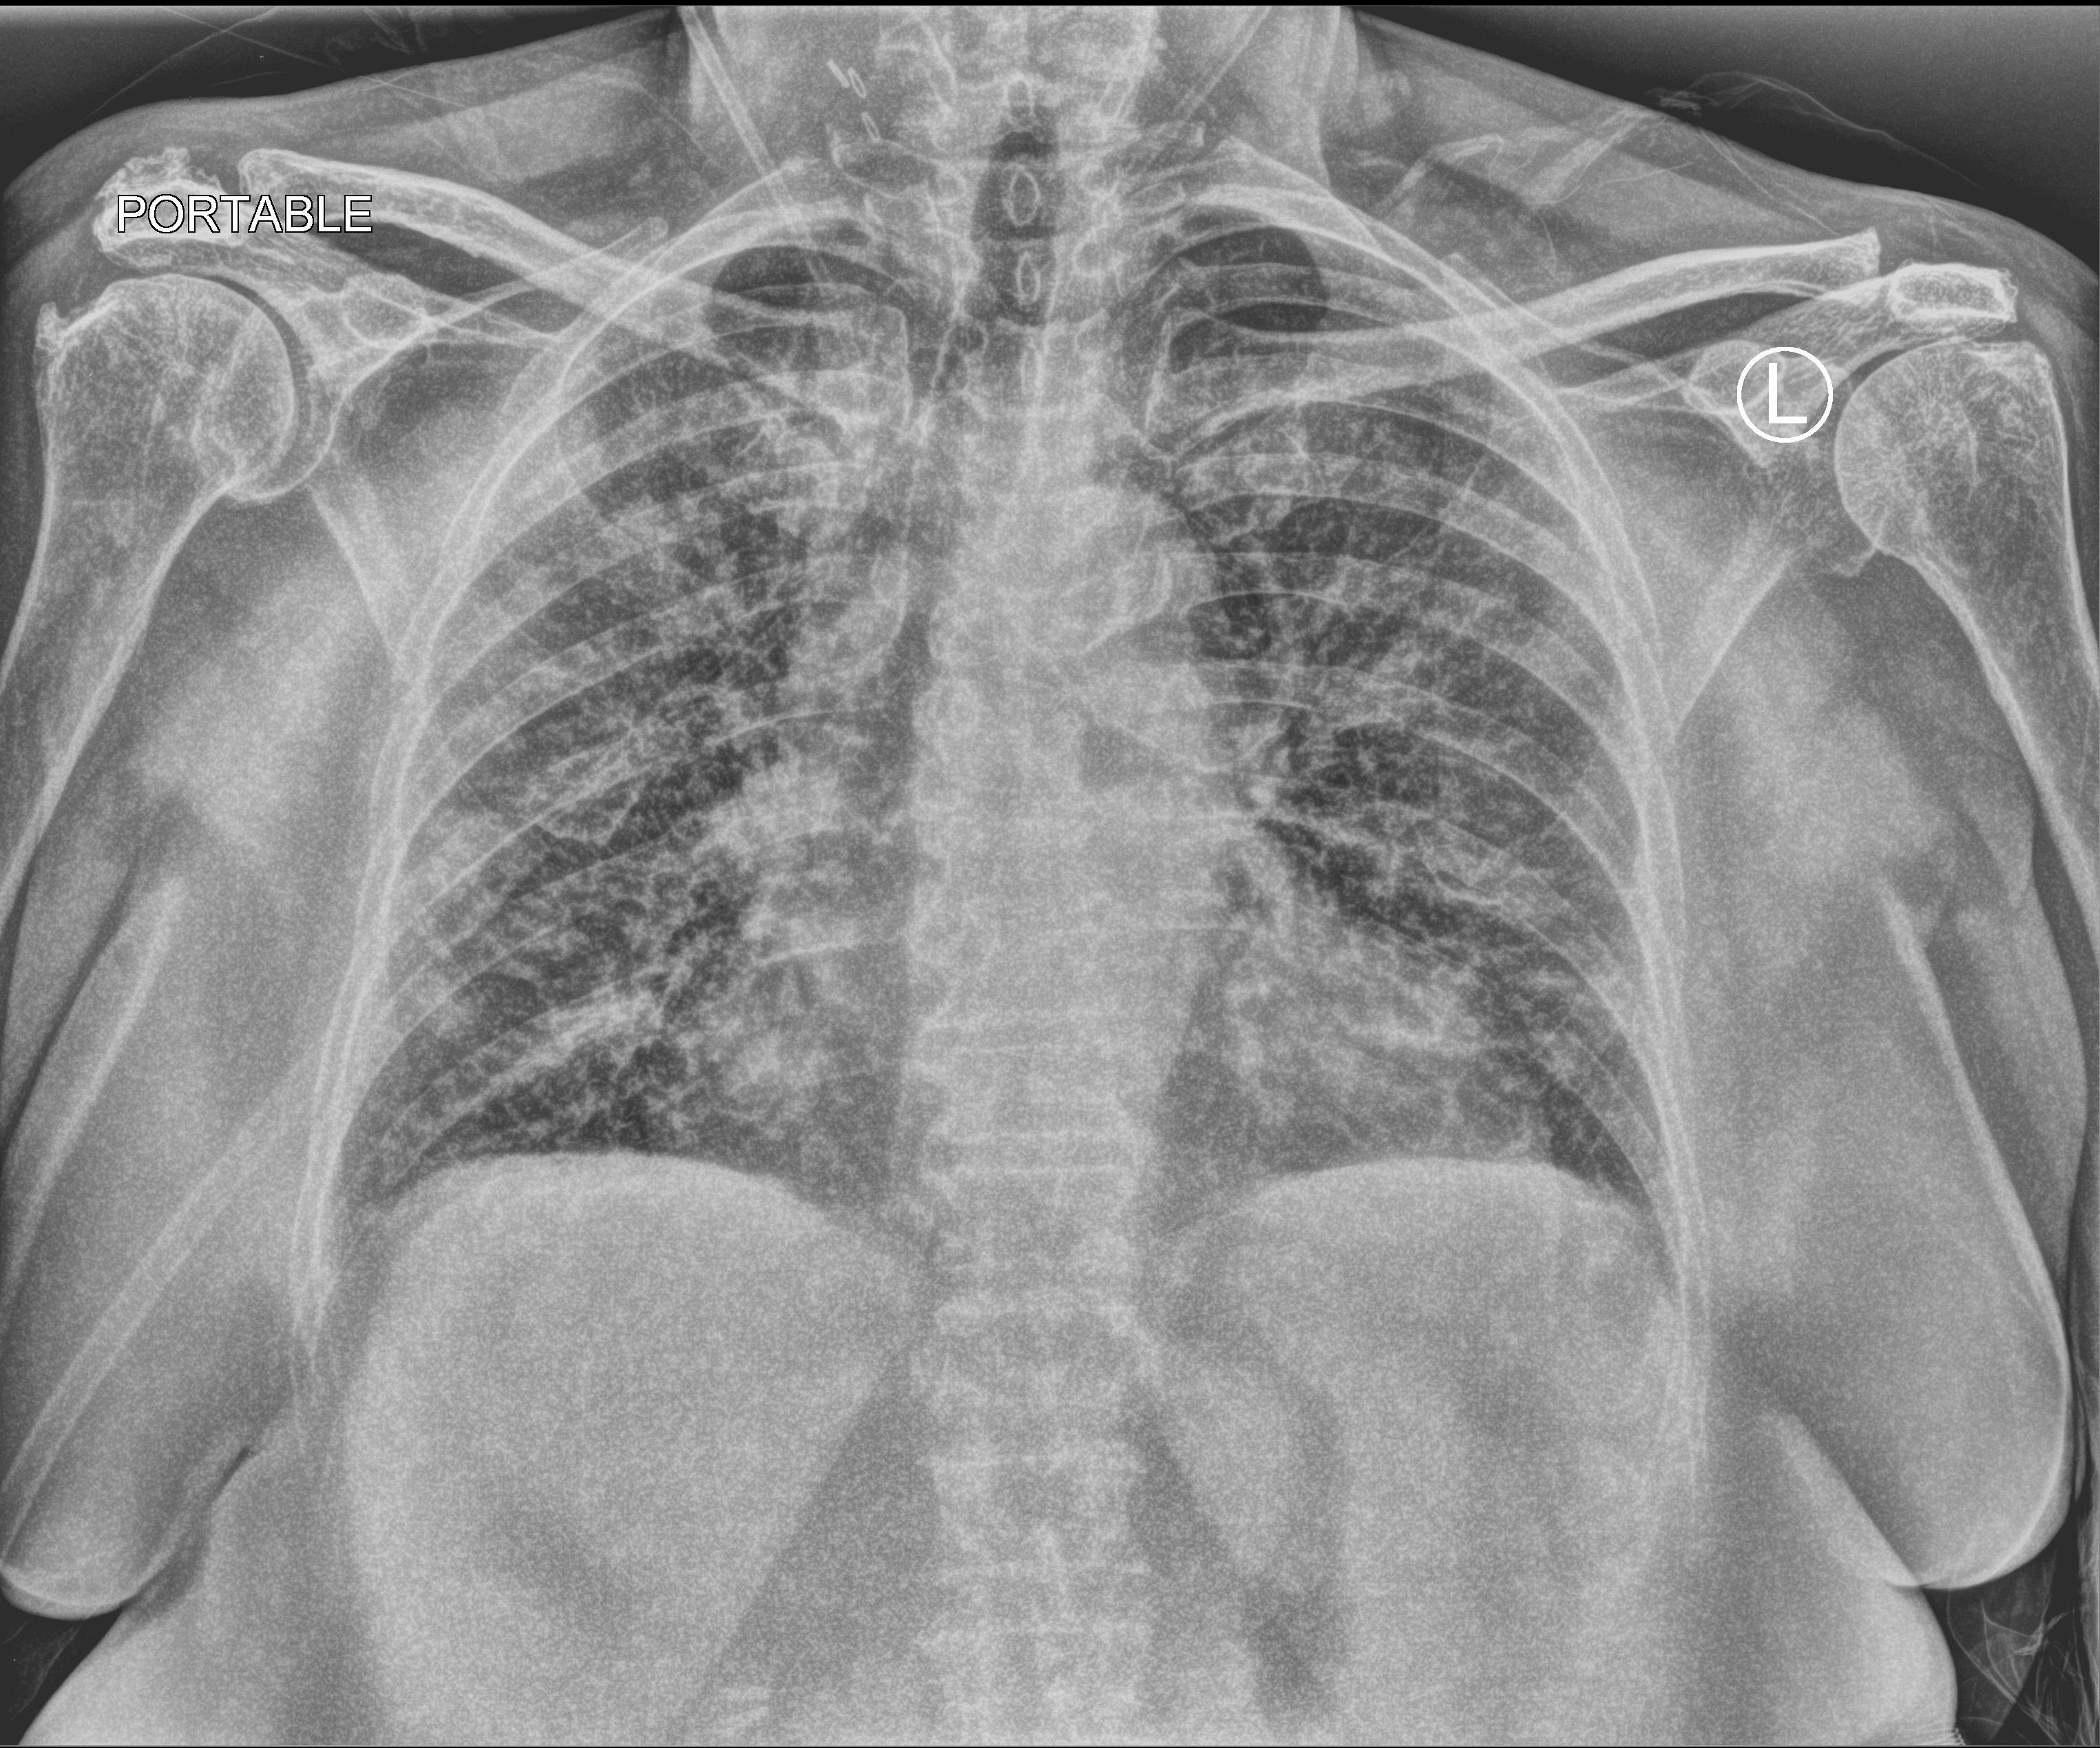
Bedside chest radiograph (computed radiography); anteroposterior (AP) projection. Female patient hospitalised with COVID-19, age 75–90 years.
From the hospital-stay record, not from the radiograph (when in the stay this image was taken is not recorded): admitted to intensive care during this hospital stay: no.